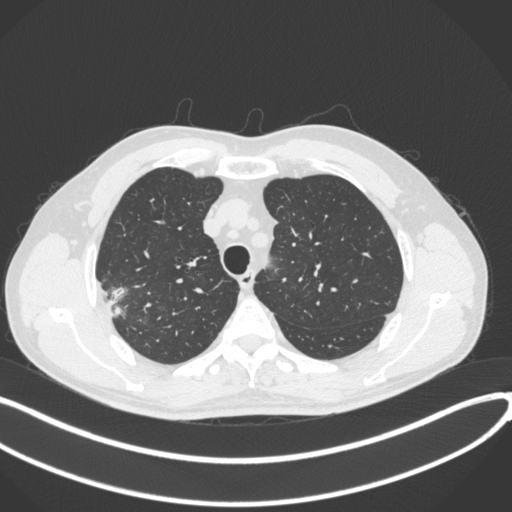
Chest CT, one axial slice. Slice 330 of 381 in the series (ordered by position). Reconstruction kernel B31f. 120 kVp. Lung window (W 1500 / L -600 HU). 512 × 512 image matrix, field of view 400 × 400 mm. Patient: male, 62 years. Case-level facts recorded for this patient, not image findings: clinical TNM (as recorded): T1c N0 M0.
Outlined on this slice (bounding box drawn by a radiologist):
- lung tumour (recorded histology: adenocarcinoma): bounding box (x1, y1, x2, y2) in pixels: (105, 281, 132, 321)